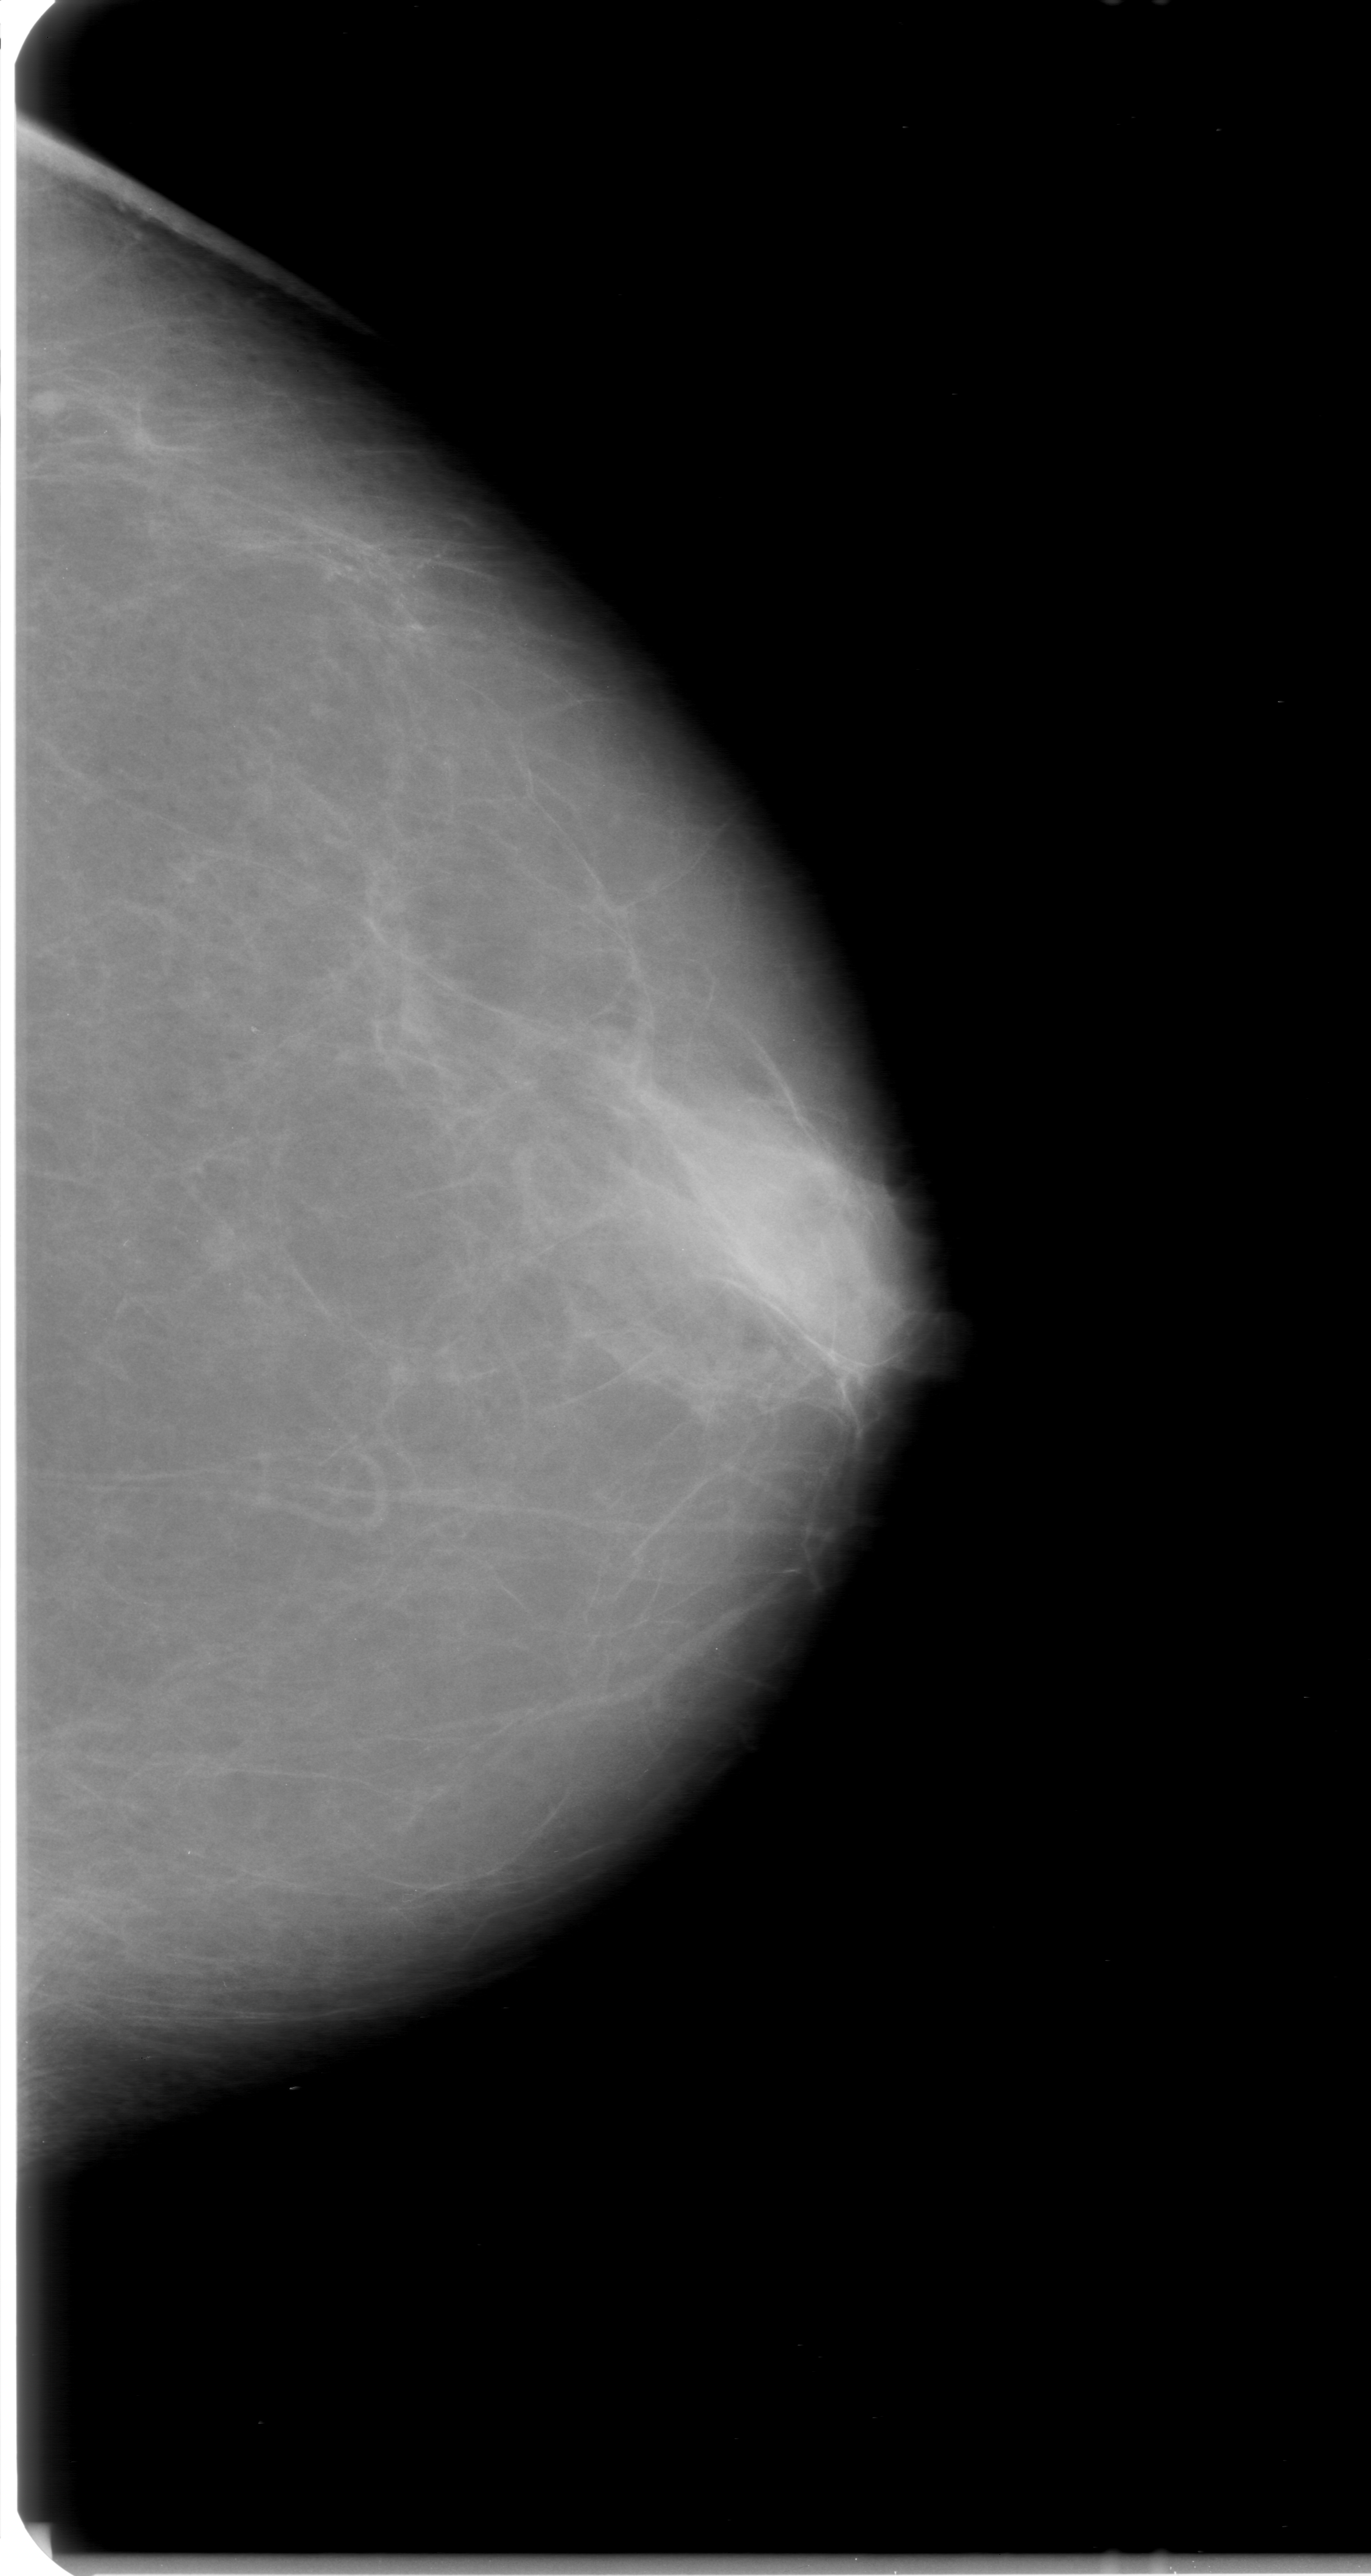
Mammogram (digitized film). Left breast. CC view. BI-RADS breast density category 1 (scale 1–4). 1371 × 2576 image matrix.
Marked abnormalities (boxes around the expert regions of interest):
- calcifications, morphology fine linear branching, distribution clustered; BI-RADS assessment category 0 (incomplete: needs additional imaging); pathology result (as recorded, not read from the image): malignant: bounding box [x1, y1, x2, y2] px = [236, 408, 526, 691]